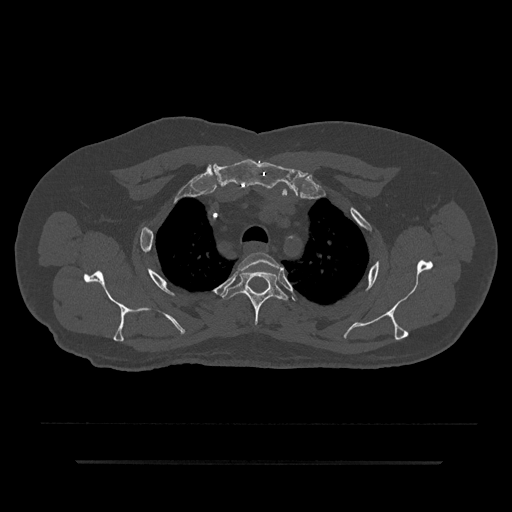
CT including the spine, one axial slice; slice 666 of 797 in the series (ordered by position); 120 kVp; bone window (W 1800 / L 400 HU); 0.5 mm slice thickness; 512 × 512 image matrix, field of view 464 × 464 mm. Male patient, age 59 years. From the clinical record (not read from this slice): primary cancer: bile ducts; vertebrae with lytic lesions (as recorded): T10.
Outlined on this slice (semi-automatic segmentation, software-assisted and operator-edited):
- T2 vertebra: bounding box [x1, y1, x2, y2] px = [238, 252, 281, 293]
- T3 vertebra: [223, 269, 288, 325]